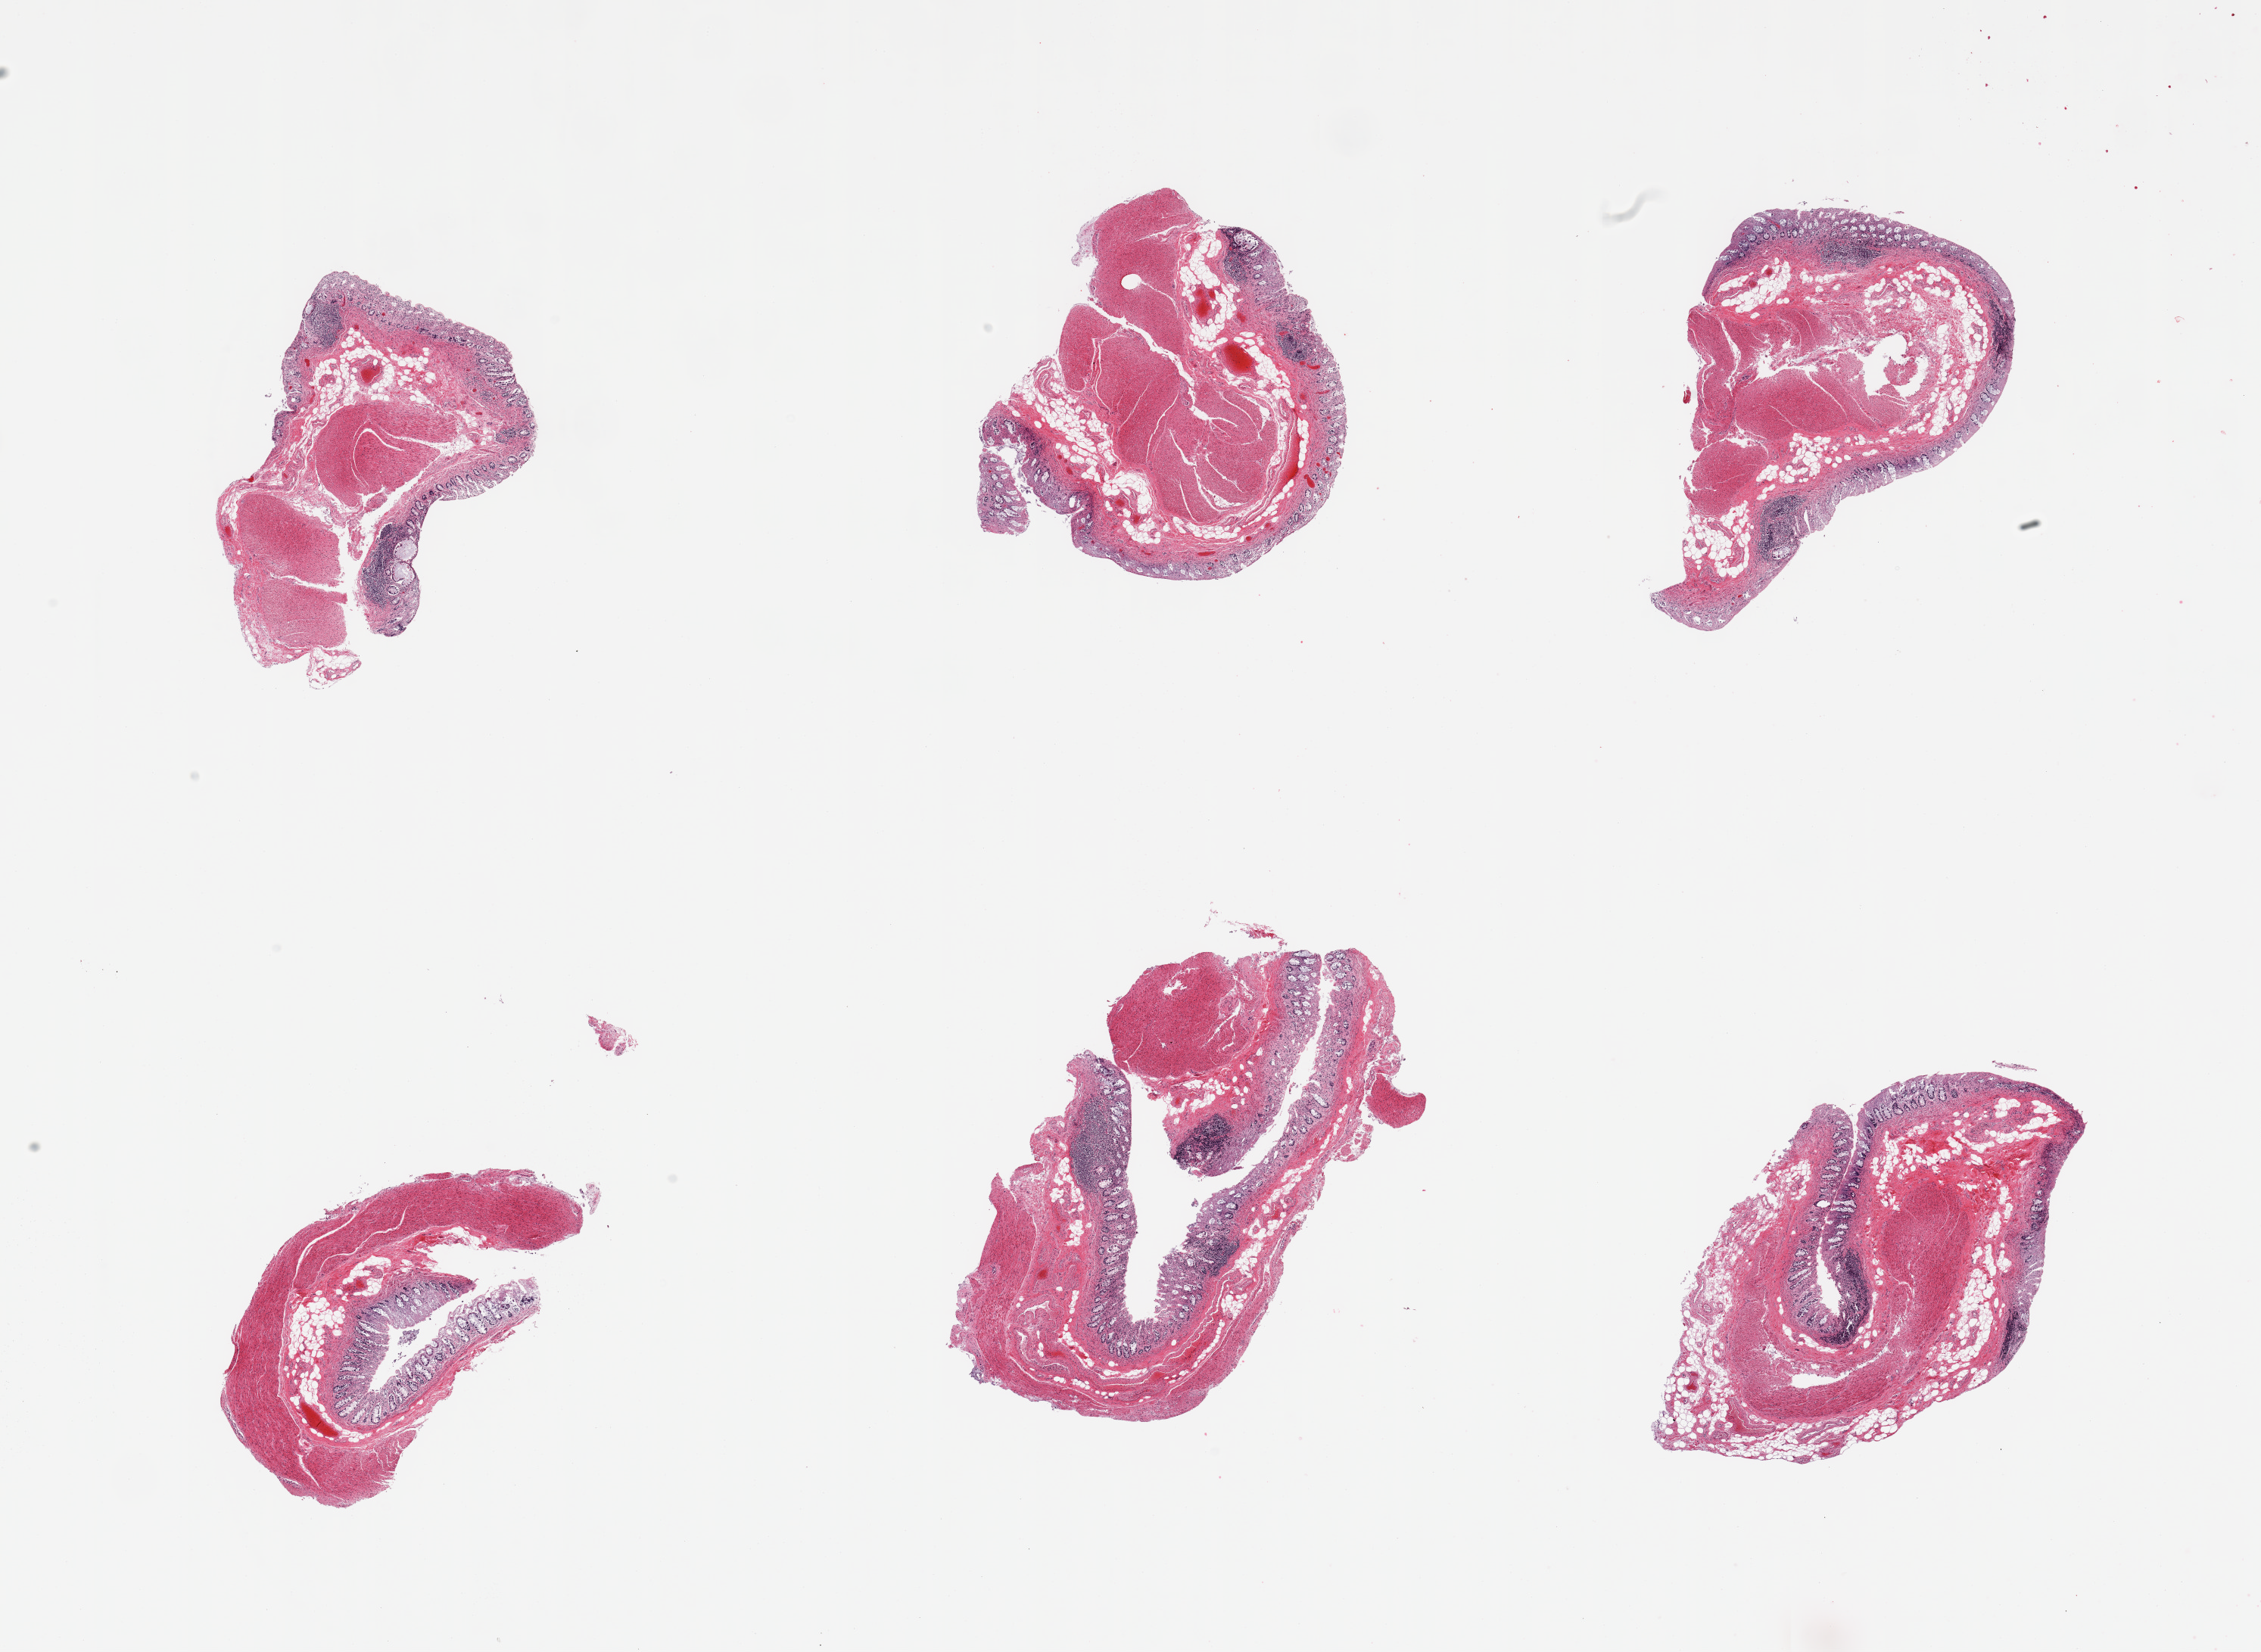
H&E whole-slide image — a low-resolution overview of the entire scanned area, about 23.6 x 17.3 mm; PAXgene-fixed, paraffin-embedded tissue; sampled site (target tissue): sigmoid colon; donor tissue sample. Donor sex: male.
• pathologist's review note for this sample: 6 pieces: all have mucosa as well as muscularis